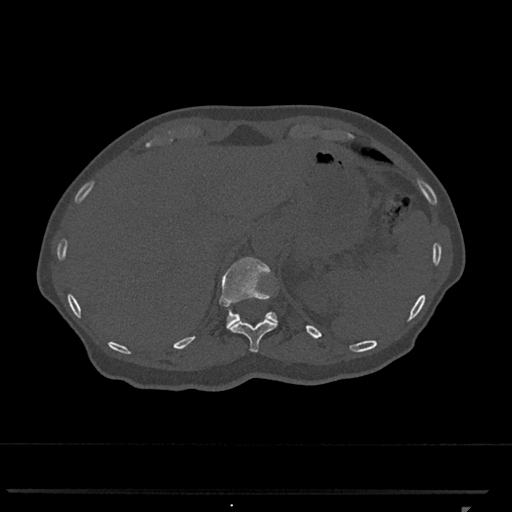
CT including the spine, one axial slice; slice 495 of 793 in the series (ordered by position); 120 kVp; bone window (W 1800 / L 400 HU); 0.5 mm slice thickness; 512 × 512 image matrix. Female patient, age 62 years. Case-level facts recorded for this patient, not image findings: primary cancer: renal.
Structures marked on this image (semi-automatic segmentation, software-assisted and operator-edited):
- T11 vertebra: bounding box <228,319,278,353> (left, top, right, bottom; pixels)
- T12 vertebra: <219,257,278,329>